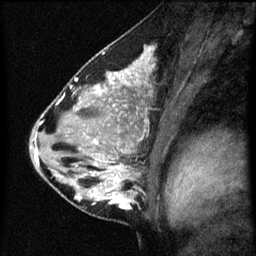
Breast MRI (dynamic contrast-enhanced), one sagittal slice; slice 34 of 60 in the series (ordered by position); dynamic contrast-enhanced series, image 2 of 3 at this slice position (ordered by acquisition); 1.5 T; TE 4.2 ms, TR 8 ms; 256 × 256 image matrix. Patient: female, 33 years.
Outlined on this slice (semi-automatic segmentation, software-assisted and operator-edited):
- analysis volume of interest (the breast-tissue region the enhancement analysis was run in; not a lesion): bounding box [x1, y1, x2, y2] px = [71, 118, 145, 215]
- tumour enhancement mask (voxels above the 70 % enhancement threshold inside the analysis volume of interest): [76, 162, 131, 209]